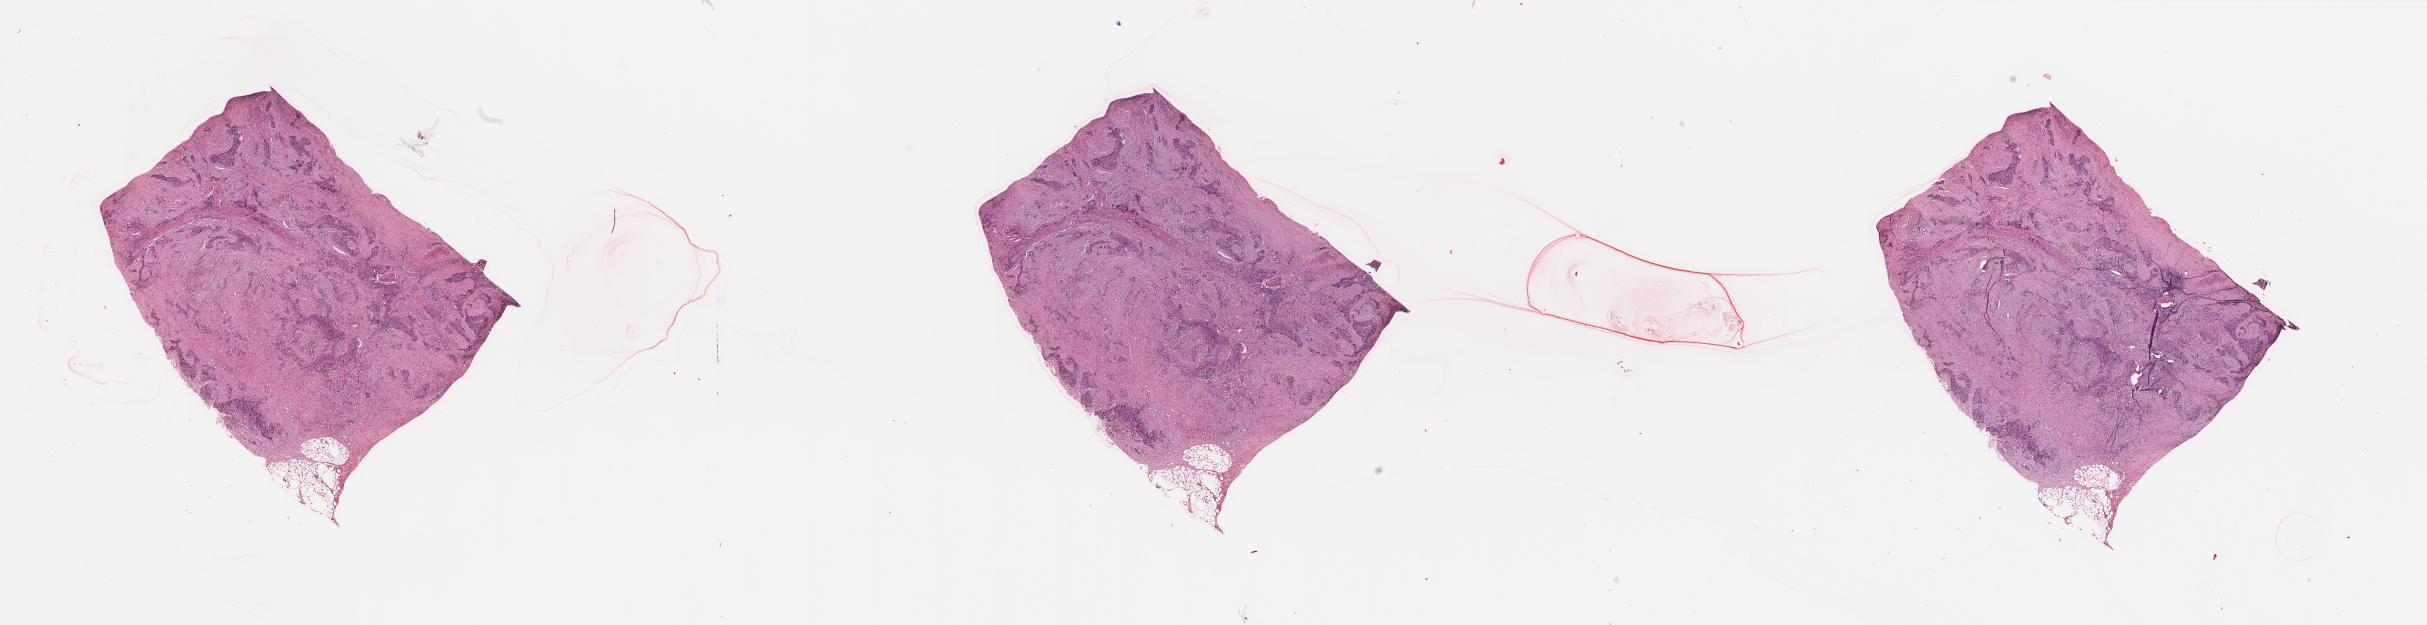
Whole-slide histology image, H&E, low-resolution overview of the scanned area, about 38.4 x 9.9 mm; tumour tissue sample, lung. Male, 73 y/o. Histologic grade: G2 (moderately differentiated).
AJCC pathologic stage: II. Primary tumour site (as recorded): right middle lobe. Histologic diagnosis: Squamous cell carcinoma, NOS.